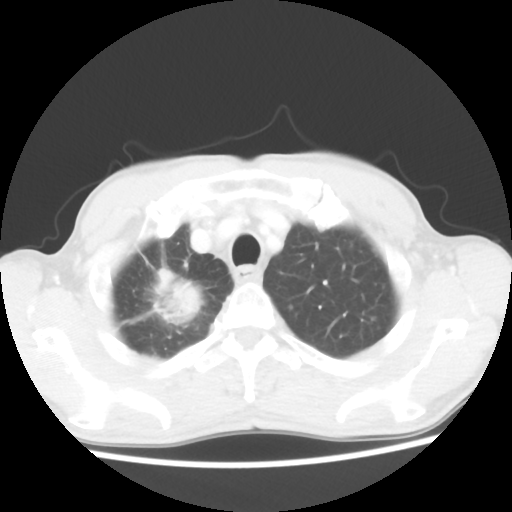
Chest CT, one axial slice. Slice 45 of 52 in the series (ordered by position). 100 kVp. Lung window (W 1500 / L -600 HU). 5 mm slice thickness. 512 × 512 image matrix, field of view 323 × 323 mm. Male patient, age 66 years. Case-level facts recorded for this patient, not image findings: clinical TNM (as recorded): T2 N0 M1a.
Outlined on this slice (bounding box drawn by a radiologist):
- lung tumour (recorded histology: adenocarcinoma): bounding box (x1, y1, x2, y2) in pixels: (143, 264, 219, 331)